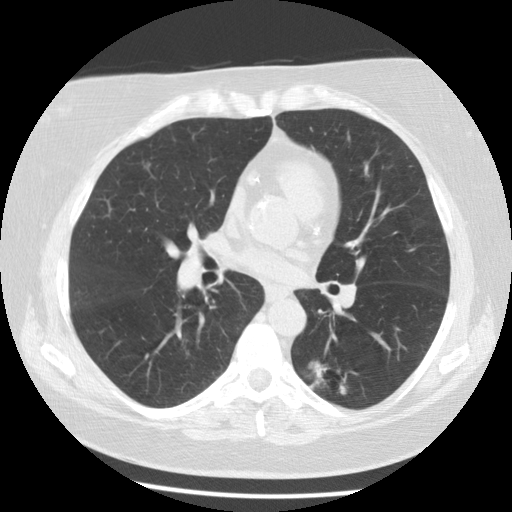
Low-dose screening chest CT, one axial slice; position 60 of 116 along the scan axis; 120 kVp; lung window (W 1500 / L -600 HU); 2.5 mm slice thickness; 512 × 512 image matrix, field of view 341 × 341 mm.
Structures marked on this image (expert manual segmentation):
- lesion 1 (tumor, lower lobe of left lung): box from (x=309, y=362) to (x=326, y=387) px